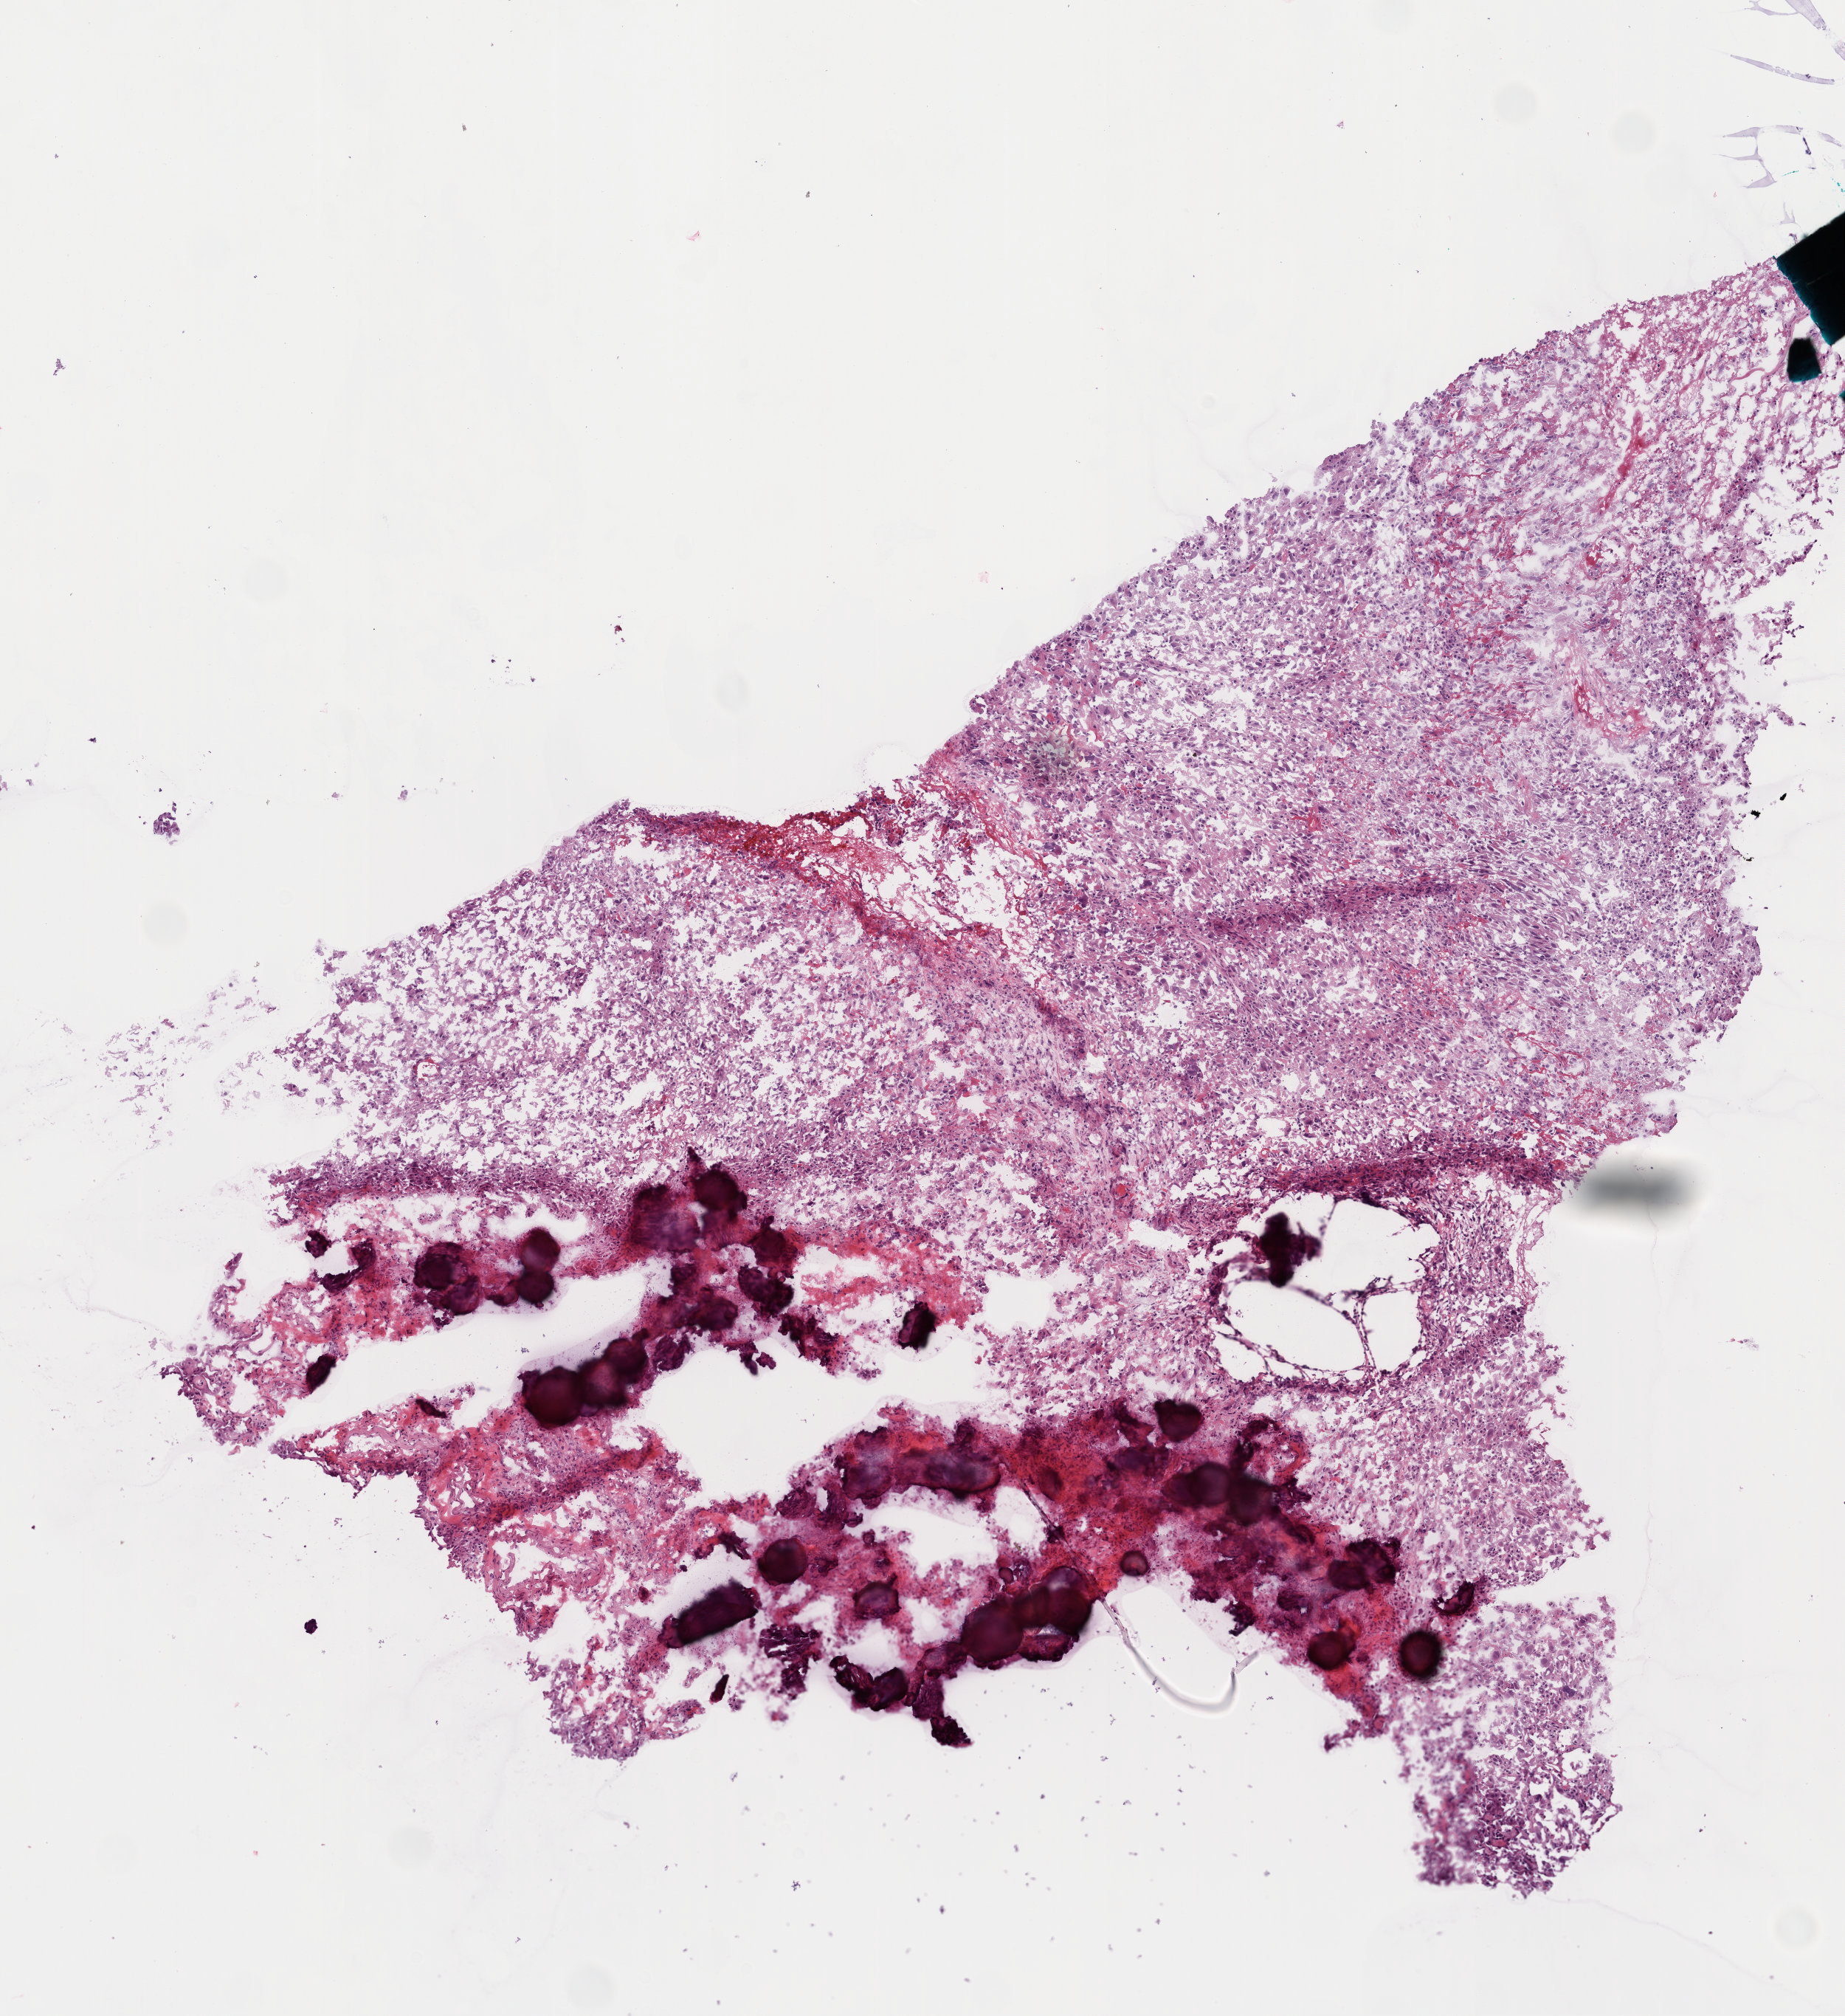
Hematoxylin and eosin (H&E) stained whole-slide image — a low-resolution overview of the entire scanned area, about 5.0 x 5.5 mm (acquisition: 20x scan); frozen section from the bottom of the tissue portion; primary tumour sample from the brain. Patient: male, age at initial diagnosis 69 years. Composition of this section per pathologist review: tumour cells 100%, tumour nuclei 100%, normal cells 0%, stromal cells 0%, necrosis 0%.
Pathologic diagnosis: Glioblastoma.